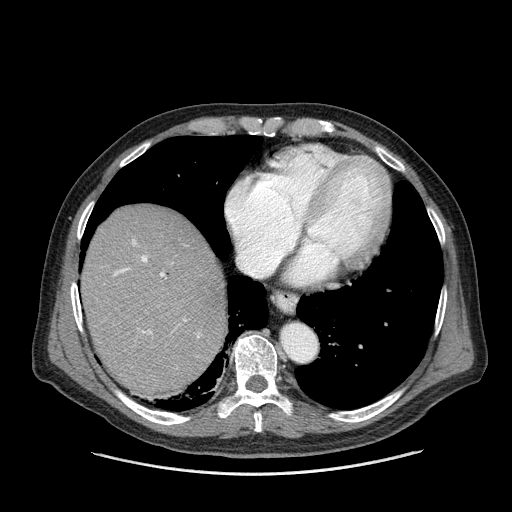
Contrast-enhanced abdominal CT (liver protocol), one axial slice. Position 134 of 180 along the scan axis. Reconstruction kernel STANDARD. One of 2 acquisitions stored at this slice position. Soft-tissue window (W 400 / L 40 HU). 512 × 512 image matrix. From the clinical record (not read from this slice): diagnosis: hepatocellular carcinoma (patient treated with transarterial chemoembolisation; whether this scan precedes or follows treatment is not stated here); TNM stage (as recorded): Stage-II; Child-Pugh class: A; tumour size: 2.8 cm.
Outlined on this slice (semi-automatic segmentation, software-assisted and operator-edited):
- abdominal aorta: bounding box (x1, y1, x2, y2) in pixels: (282, 324, 317, 361)
- liver parenchyma outside the tumour (the mass and vessels are separate outlines, so this box may not span the whole liver): (82, 204, 226, 398)
- liver vessels: (114, 239, 200, 337)